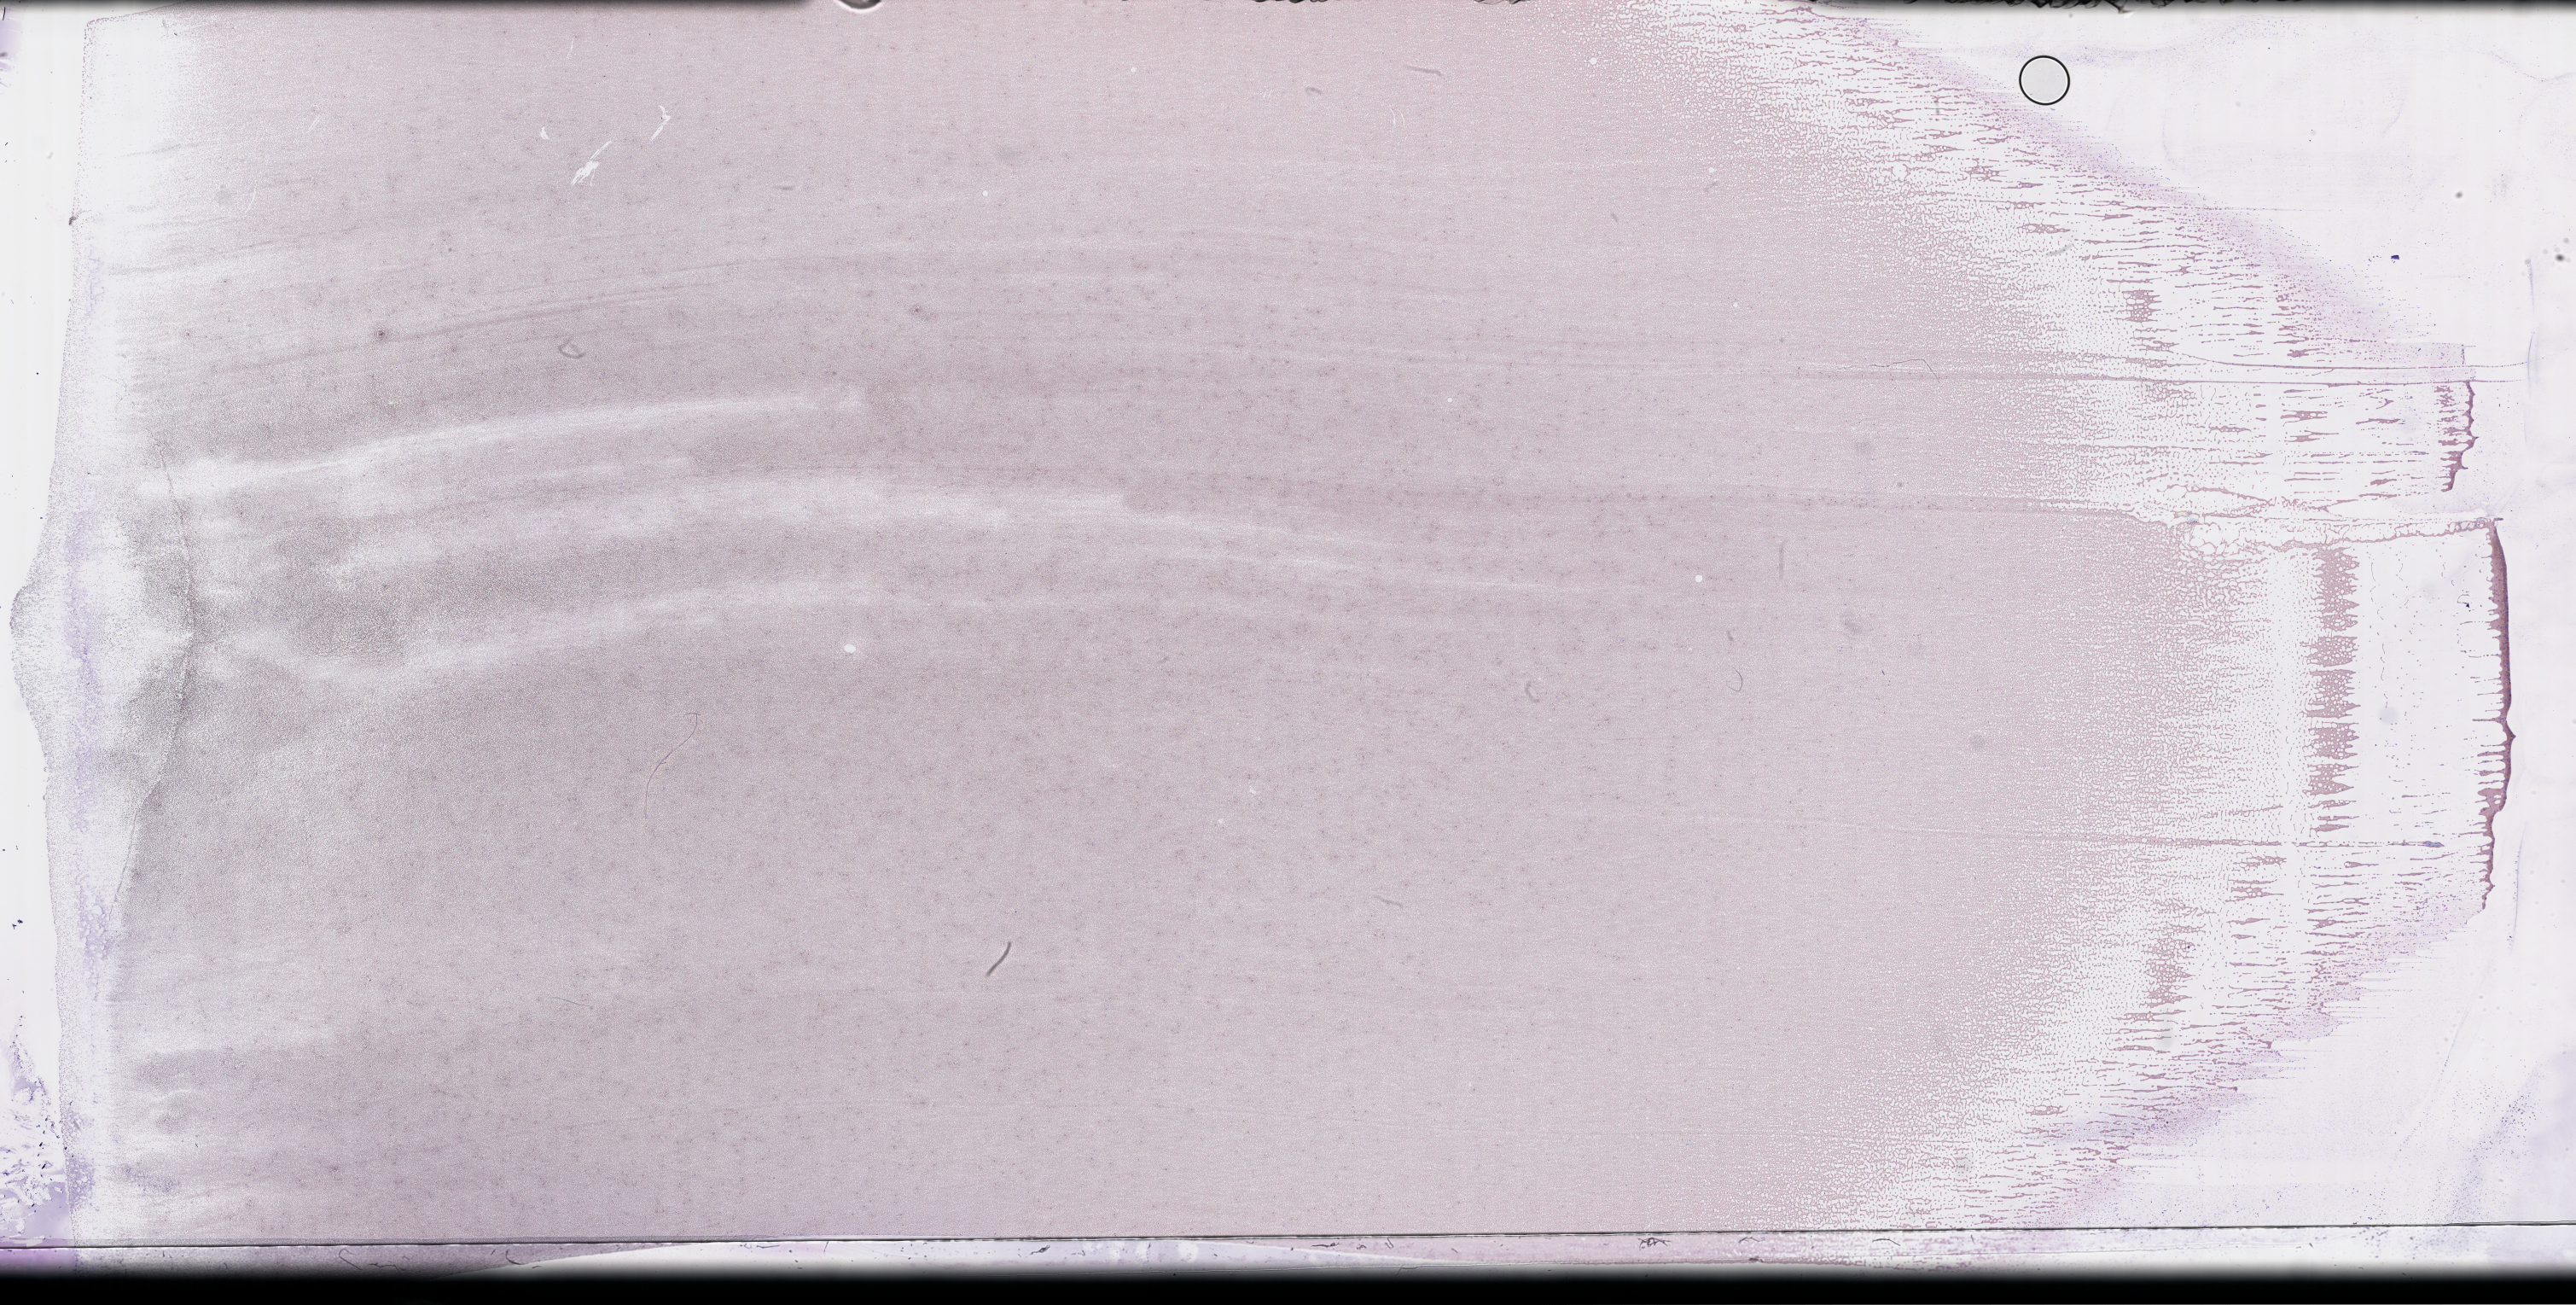
Whole-slide image of a whole blood smear, Wright-Giemsa stain — shown as a low-resolution overview of the whole scanned area (about 48.8 x 24.7 mm); smear from an EDTA sample; specimen time point: collected on treatment. Patient sex: female.
* patient diagnosis: Plasma Cell Myeloma